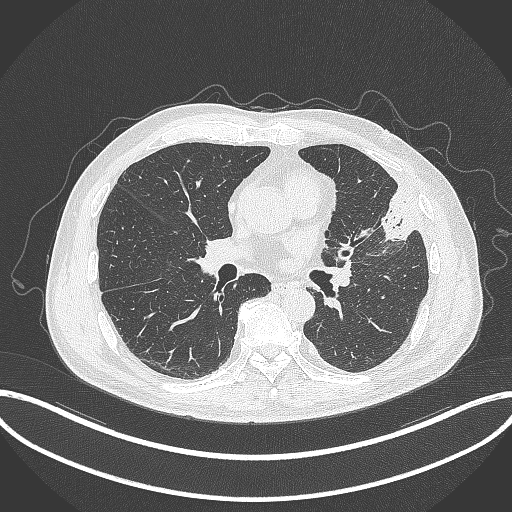
Chest CT, one axial slice. Slice 171 of 382 in the series (ordered by position). Reconstruction kernel B70f. 120 kVp. Lung window (W 1500 / L -600 HU). 1 mm slice thickness. 512 × 512 image matrix. Patient: male, 64 years. From the clinical record (not read from this slice): clinical TNM (as recorded): T4 N1 M0; histopathological grade: G3.
Outlined on this slice (bounding box drawn by a radiologist):
- lung tumour (recorded histology: adenocarcinoma): box from (x=376, y=179) to (x=419, y=245) px